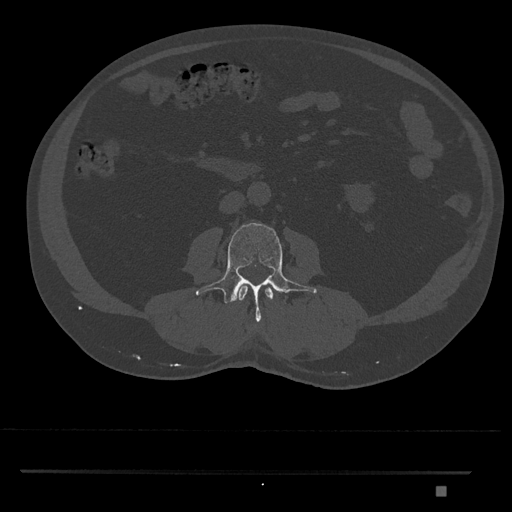
CT including the spine, one axial slice. Slice 692 of 1134 in the series (ordered by position). Reconstruction kernel Br40s/3. 120 kVp. Bone window (W 1800 / L 400 HU). 0.5 mm slice thickness. 512 × 512 image matrix. Male patient, age 65 years. From the clinical record (not read from this slice): primary cancer: prostate.
Outlined on this slice (semi-automatically segmented with operator editing):
- L2 vertebra: bounding box <237,286,273,301> (left, top, right, bottom; pixels)
- L3 vertebra: <196,222,317,321>